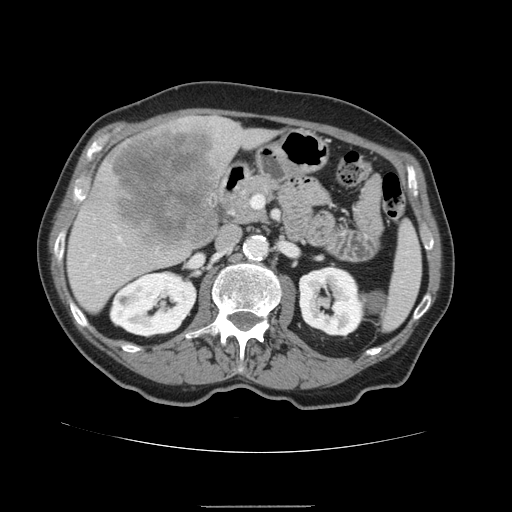
Contrast-enhanced abdominal CT, one axial slice. Position 72 of 168 along the scan axis. Intravenous contrast given. Soft-tissue window (W 400 / L 40 HU). 2.5 mm slice thickness. 512 × 512 image matrix, field of view 386 × 386 mm. Male patient, age 74 years. From the clinical record (not read from this slice): diagnosis: colorectal cancer liver metastases, imaged before liver resection; multiple liver metastases: no; largest metastasis: 14.5 cm; disease in both lobes: yes.
Structures marked on this image (expert manual segmentation):
- liver: bounding box [x1, y1, x2, y2] px = [66, 116, 278, 314]
- planned liver remnant (the part of the liver to remain after resection): [67, 127, 278, 314]
- liver metastasis: [112, 130, 220, 248]